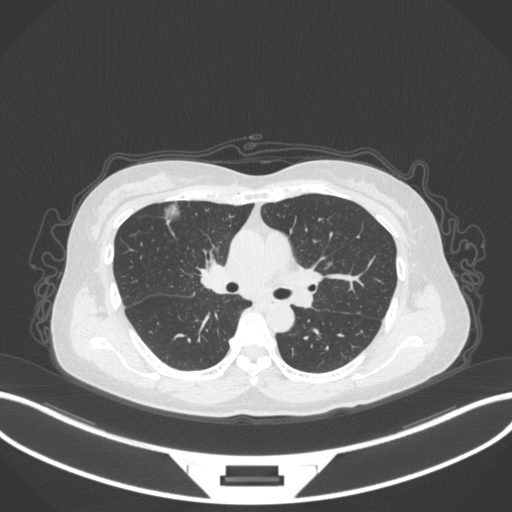
Chest CT, one axial slice. Position 198 of 317 along the scan axis. Reconstruction kernel B31f. 120 kVp. Lung window (W 1500 / L -600 HU). 512 × 512 image matrix. Female patient, age 61 years. Case-level facts recorded for this patient, not image findings: clinical TNM (as recorded): T1b N0 M0; histopathological grade: G1.
Outlined on this slice (bounding box drawn by a radiologist):
- lung tumour (recorded histology: adenocarcinoma): bounding box <160,196,183,227> (left, top, right, bottom; pixels)